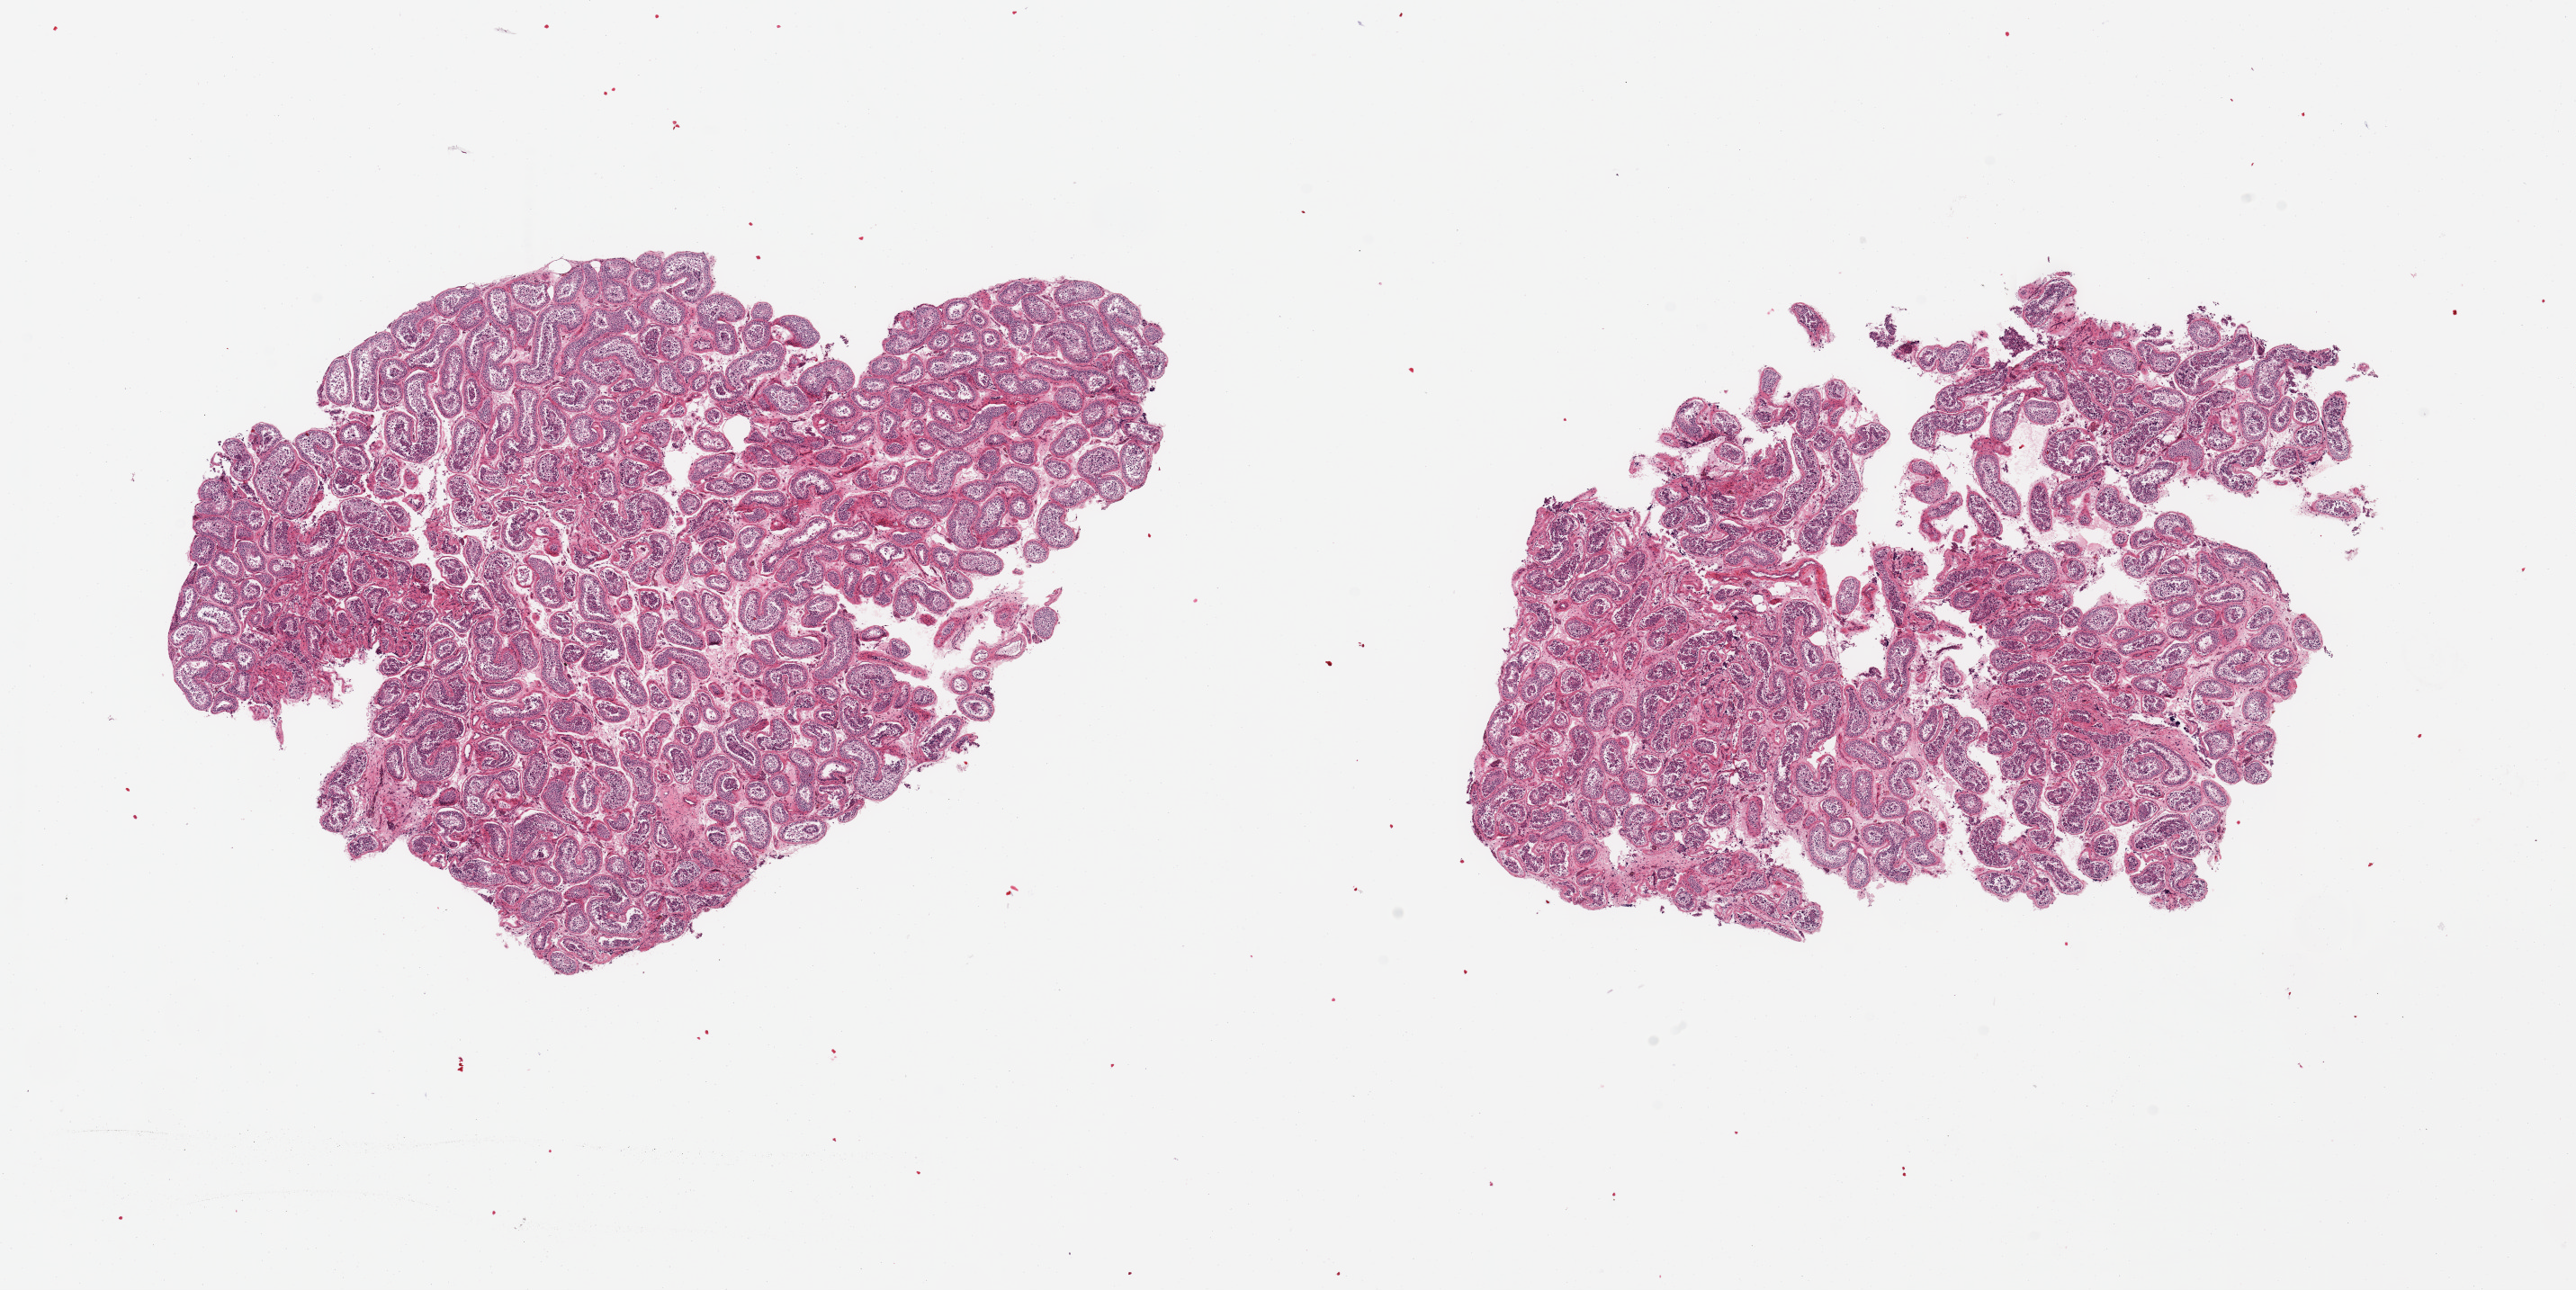
Whole-slide image, haematoxylin and eosin stain, a low-resolution overview of the entire scanned area, about 22.6 x 11.3 mm, PAXgene-fixed paraffin-embedded (PFPE) section, target tissue: testis, tissue donor sample. Donor sex: male.
Review note (as recorded): 2 pieces, spermatogenesis present; appears reduced.